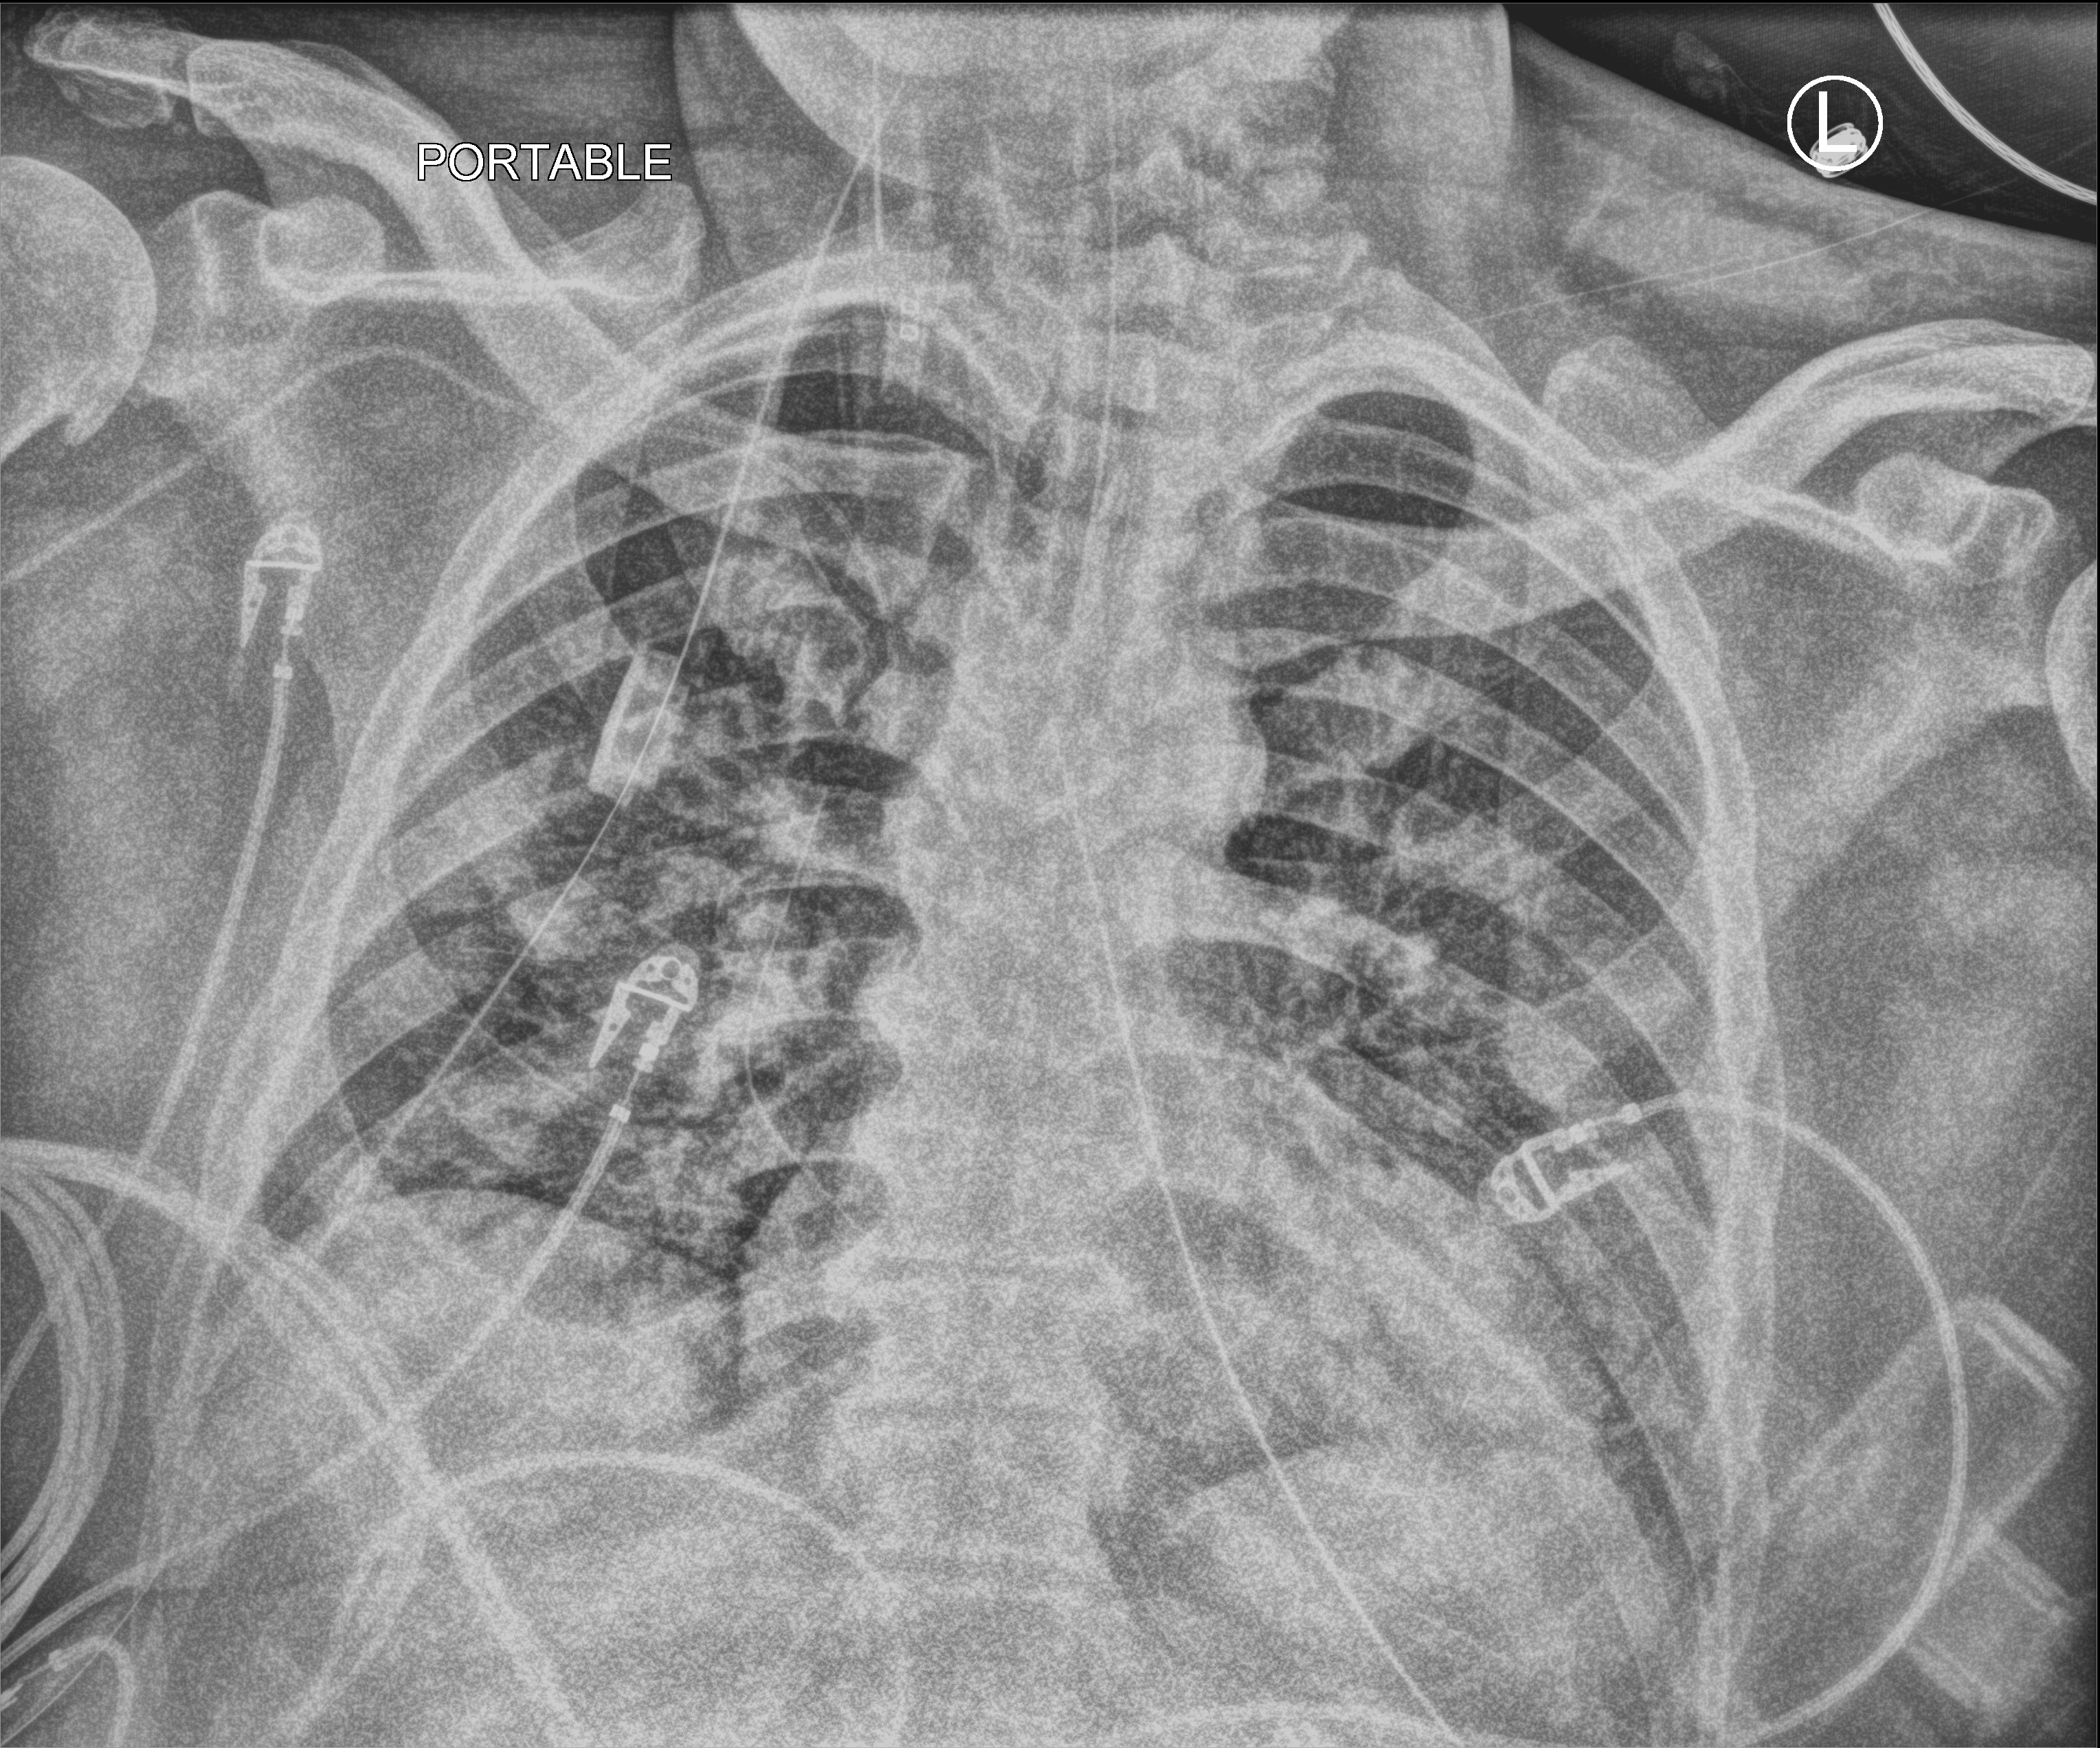
Portable chest radiograph; anteroposterior (AP) projection. Male patient hospitalised with COVID-19, age 18–59 years.
From the hospital-stay record, not from the radiograph (when in the stay this image was taken is not recorded): COPD (admission record): no; mechanically ventilated during this hospital stay: yes; admitted to intensive care during this hospital stay: yes.